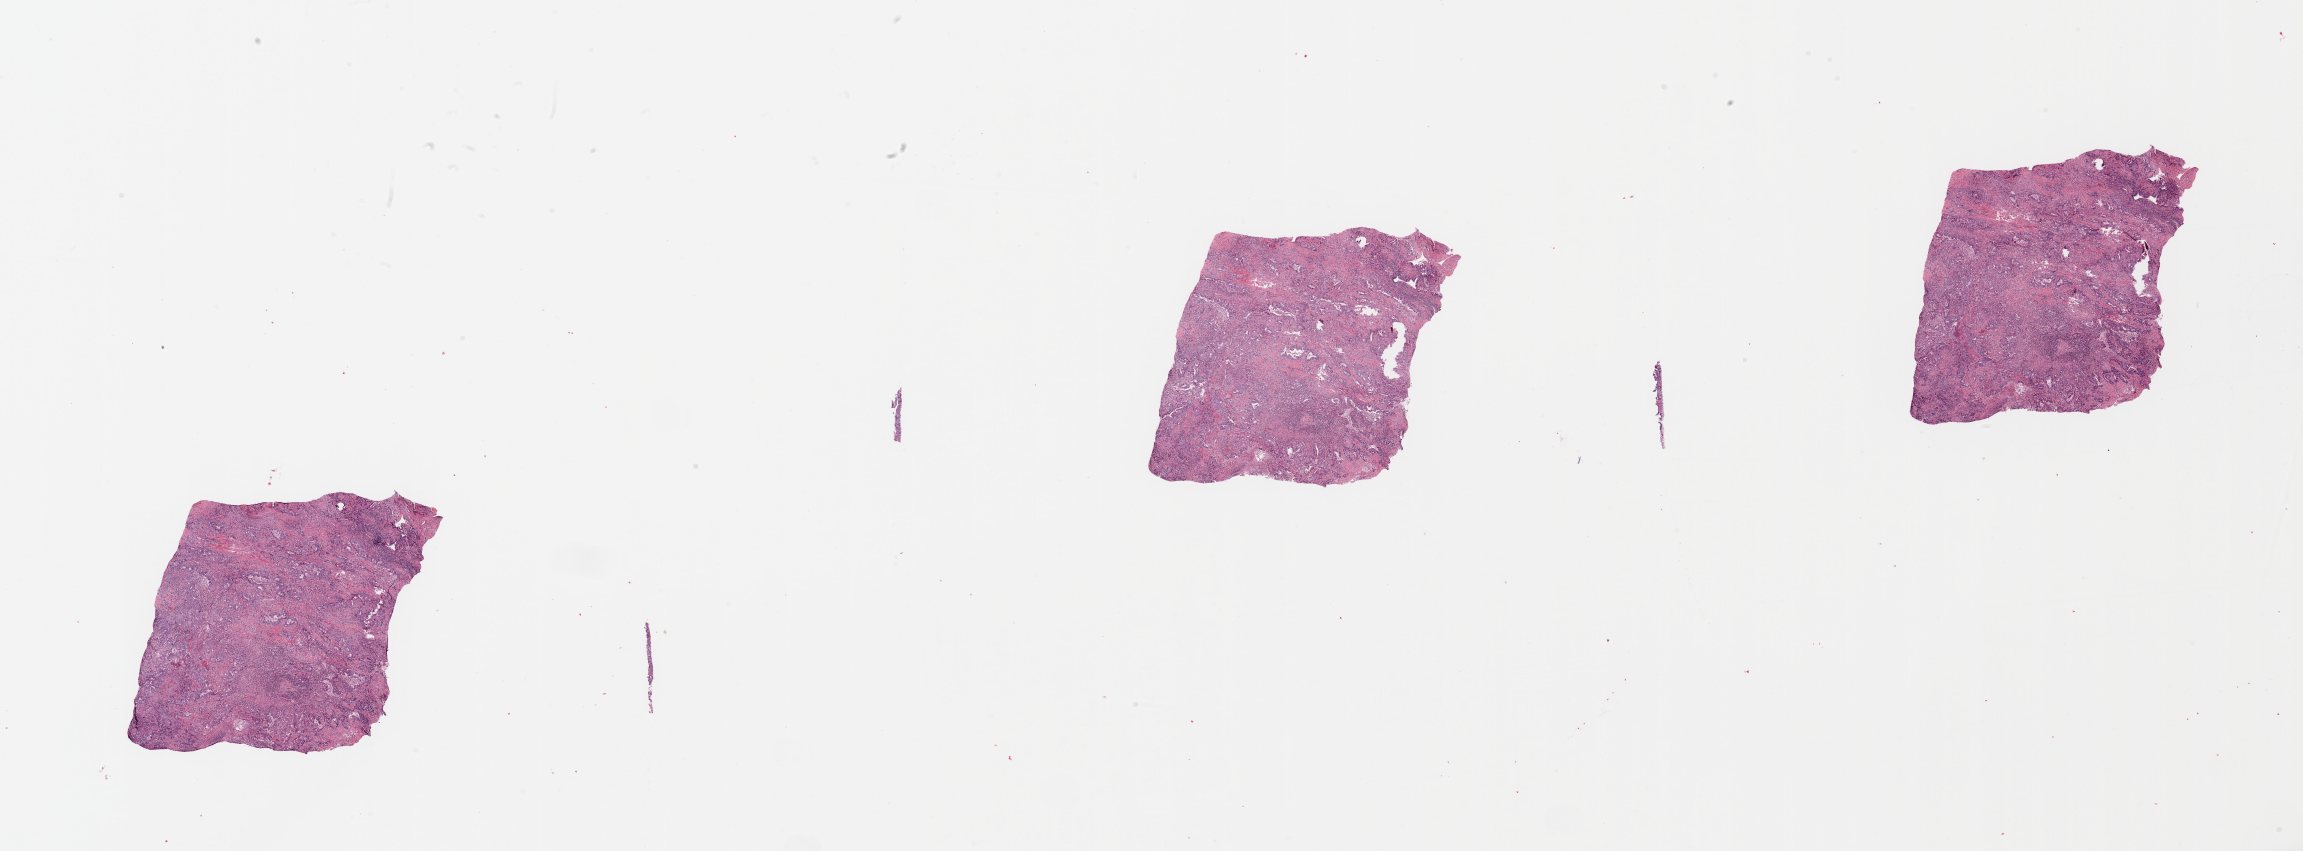
Whole-slide histology image, H&E — a low-resolution overview of the entire scanned area, about 36.4 x 13.5 mm (slide scanned at 20x), tumour tissue sample, sampled site: pancreas. Patient: female, age 60 years. Histologic grade: G2 (moderately differentiated). Slide review estimates, as recorded: tumour nuclei 60%, necrosis 0%.
AJCC pathologic stage: IIB. Primary tumour site (as recorded): head. Diagnosis: Infiltrating duct carcinoma, NOS.